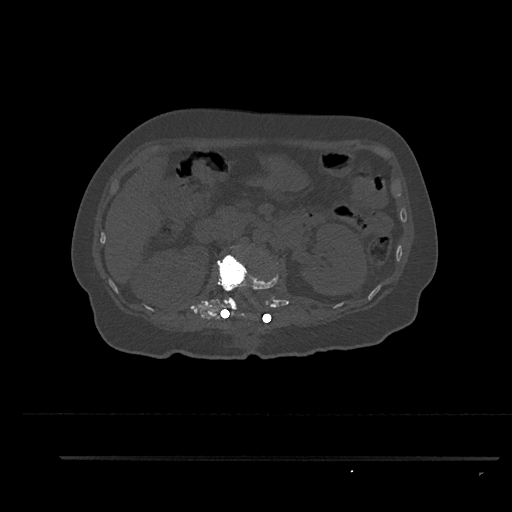
CT including the spine, one axial slice; slice 201 of 797 in the series (ordered by position); bone window (W 1800 / L 400 HU); 512 × 512 image matrix, field of view 408 × 408 mm. Patient: female, 44 years. From the clinical record (not read from this slice): primary cancer: renal; vertebrae with lytic lesions (as recorded): L1.
Structures marked on this image (semi-automatic segmentation, software-assisted and operator-edited):
- L1 vertebra: bounding box <217,245,278,318> (left, top, right, bottom; pixels)